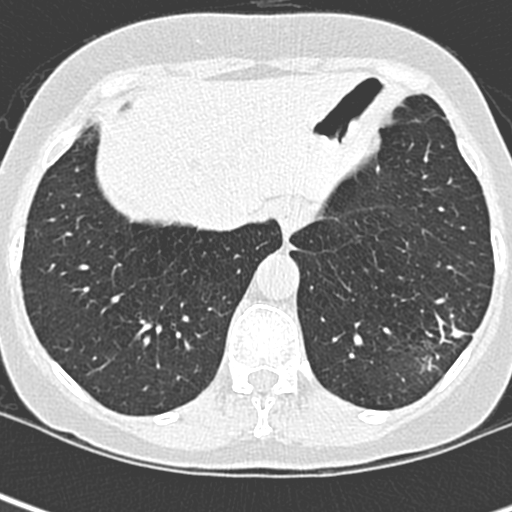
Low-dose screening chest CT, one axial slice; position 67 of 252 along the scan axis; 120 kVp; lung window (W 1500 / L -600 HU); 512 × 512 image matrix.
Structures marked on this image (expert manual segmentation):
- lesion 1 (tumor, lower lobe of left lung): bounding box (x1, y1, x2, y2) in pixels: (422, 322, 466, 371)